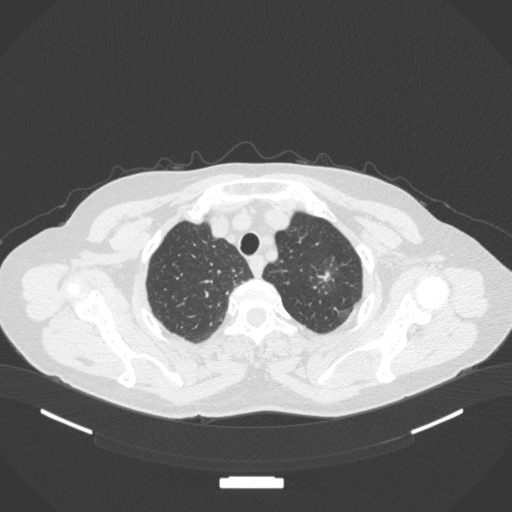
Chest CT, one axial slice. Position 311 of 369 along the scan axis. 120 kVp. Lung window (W 1500 / L -600 HU). 1 mm slice thickness. 512 × 512 image matrix, field of view 400 × 400 mm. Female patient, age 64 years. From the clinical record (not read from this slice): clinical TNM (as recorded): T1c N0 M0; histopathological grade: G1.
Structures marked on this image (rectangle marked by the reading radiologist):
- lung tumour (recorded histology: adenocarcinoma): bounding box (x1, y1, x2, y2) in pixels: (307, 248, 347, 300)